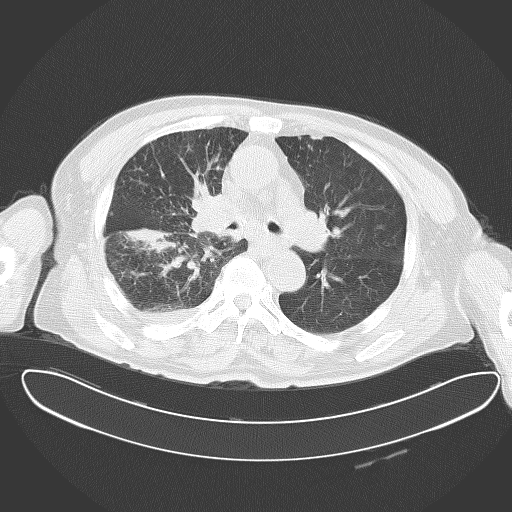
Chest CT, one axial slice. Slice 36 of 62 in the series (ordered by position). 120 kVp. Lung window (W 1500 / L -600 HU). 5 mm slice thickness. 512 × 512 image matrix, field of view 427 × 427 mm. Male patient, age 78 years. Case-level facts recorded for this patient, not image findings: clinical TNM (as recorded): T2 N1 M1.
Structures marked on this image (rectangle marked by the reading radiologist):
- lung tumour (recorded histology: adenocarcinoma): bounding box (x1, y1, x2, y2) in pixels: (122, 192, 237, 275)